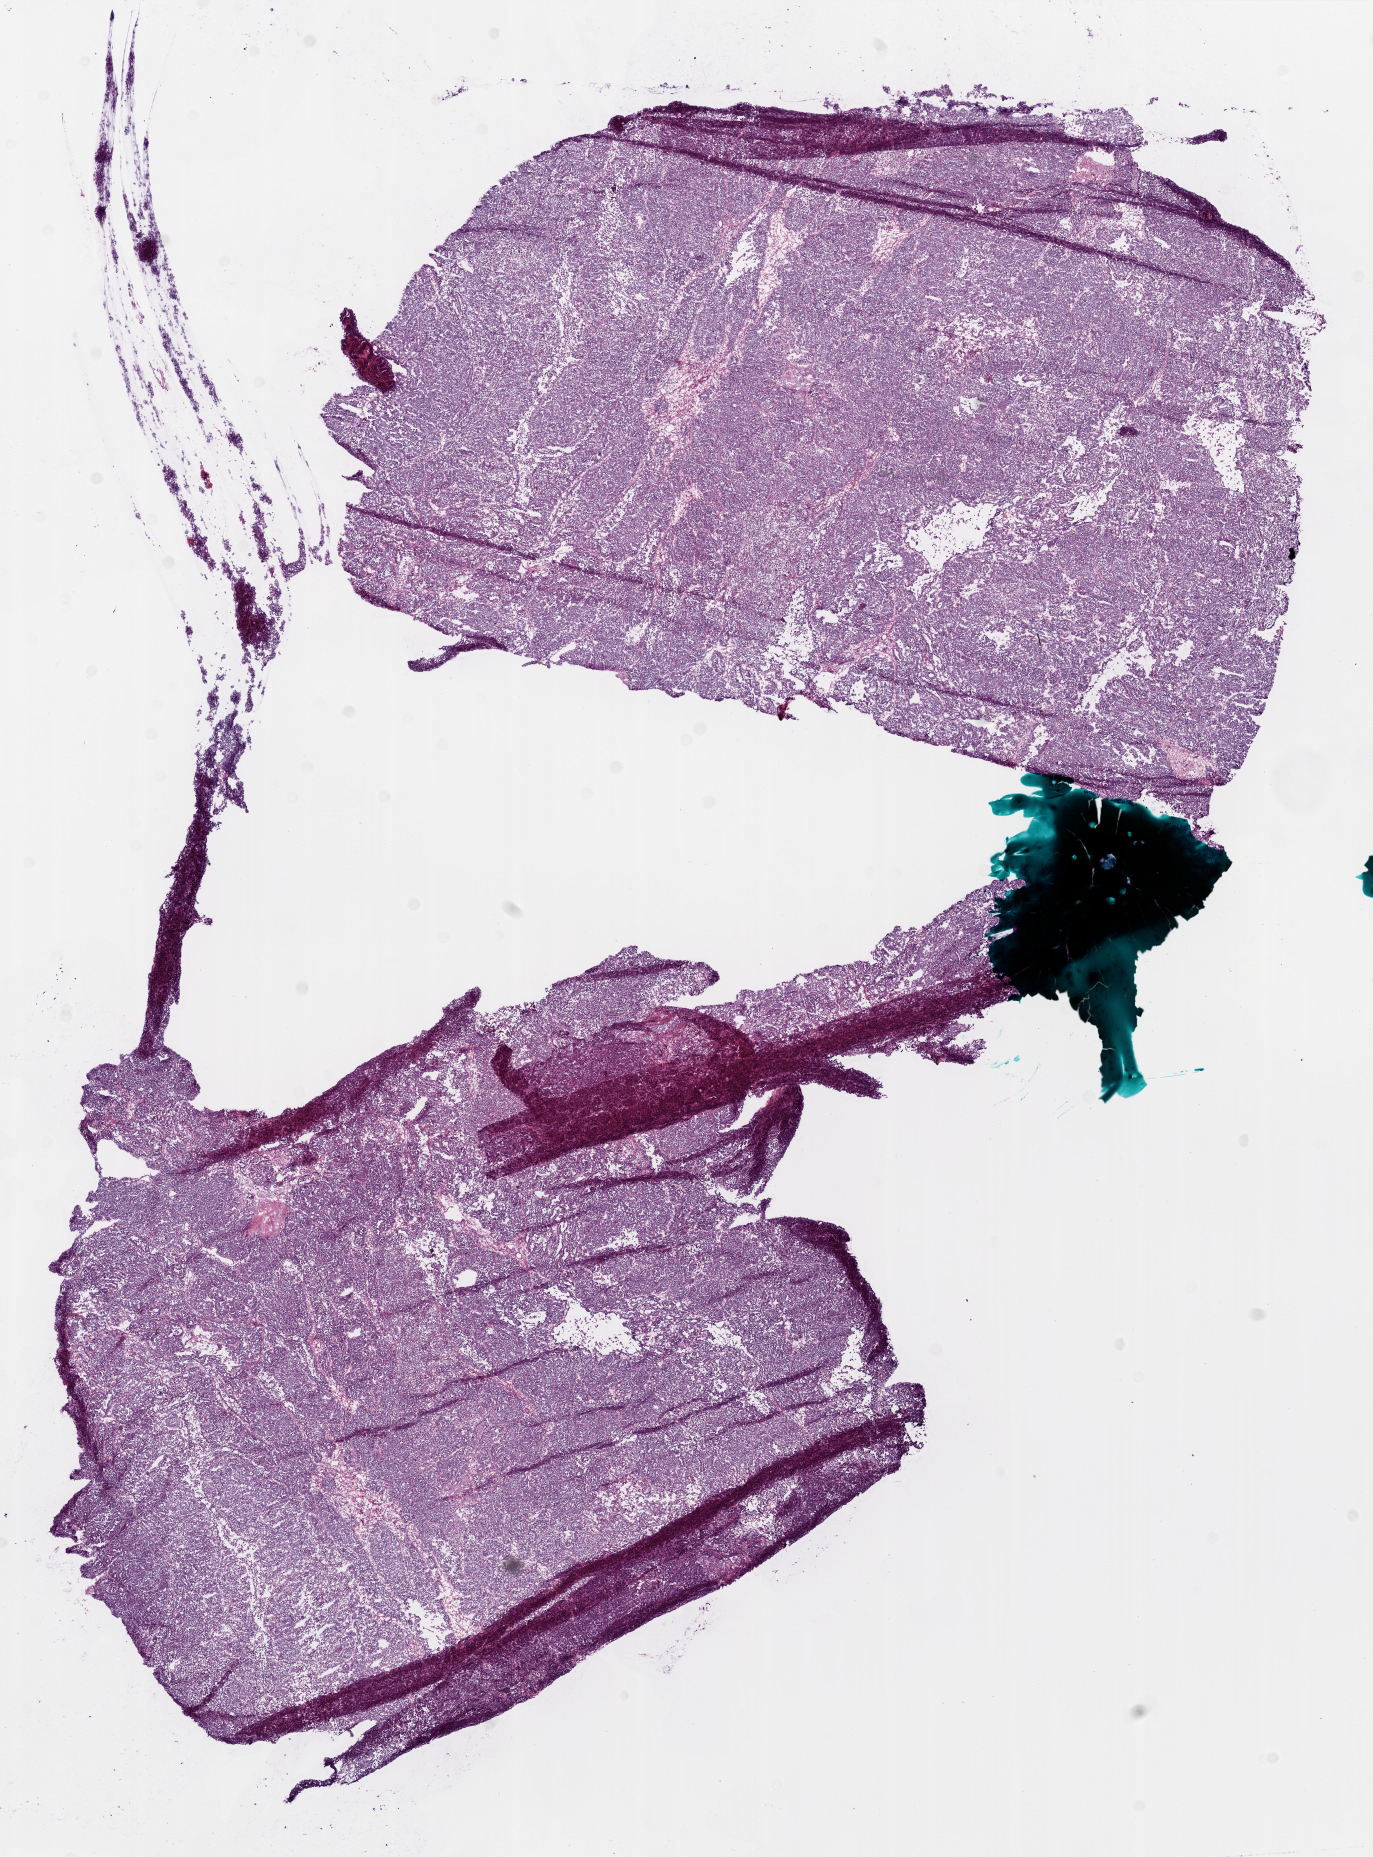
Digitized Hematoxylin and eosin (H&E) stained tissue section (whole slide), shown as a low-resolution overview of the whole scanned area (about 11.0 x 14.9 mm, acquisition: 20x scan). Frozen section from the bottom of the tissue portion. Primary tumour sample from the ovary. Female patient; age at initial diagnosis 59 years. Composition of this section per pathologist review: tumour cells 0%, tumour nuclei 95%.
Histologic diagnosis: Serous cystadenocarcinoma, NOS.